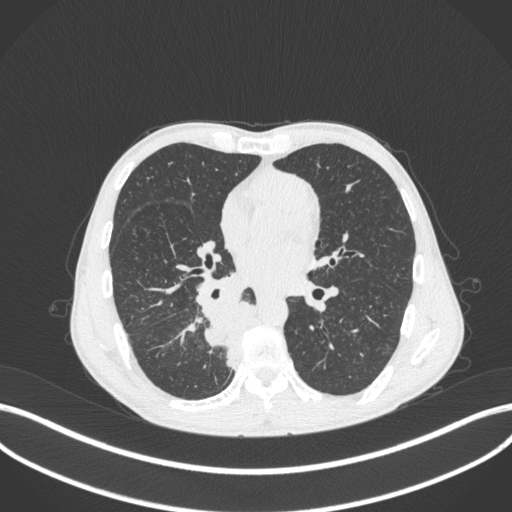
Chest CT, one axial slice. Position 183 of 371 along the scan axis. Reconstruction kernel B31f. 120 kVp. Lung window (W 1500 / L -600 HU). 1 mm slice thickness. 512 × 512 image matrix. Patient: male, 58 years. Case-level facts recorded for this patient, not image findings: clinical TNM (as recorded): T3 N1 M1.
Outlined on this slice (bounding box drawn by a radiologist):
- lung tumour (recorded histology: squamous cell carcinoma): bounding box [x1, y1, x2, y2] px = [198, 300, 264, 371]